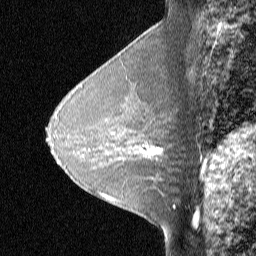
Breast MRI (dynamic contrast-enhanced), one sagittal slice; position 30 of 48 along the scan axis; dynamic contrast-enhanced study with each time point stored as its own series, time point 2 of 3 at this slice position (early post-contrast, ordered by acquisition time); 1.5 T; TE 4 ms, TR 30 ms; 256 × 256 image matrix, field of view 180 × 180 mm. Female patient, age 31 years. From the clinical record (not read from this slice): setting: breast cancer imaged before/during neoadjuvant chemotherapy; receptor status: HER2-positive.
Outlined on this slice (semi-automatically segmented with operator editing):
- analysis volume of interest (the breast-tissue region the enhancement analysis was run in; not a lesion): bounding box [x1, y1, x2, y2] px = [129, 130, 175, 167]
- tumour enhancement mask (voxels above the 90 % enhancement threshold inside the analysis volume of interest): [142, 145, 162, 155]